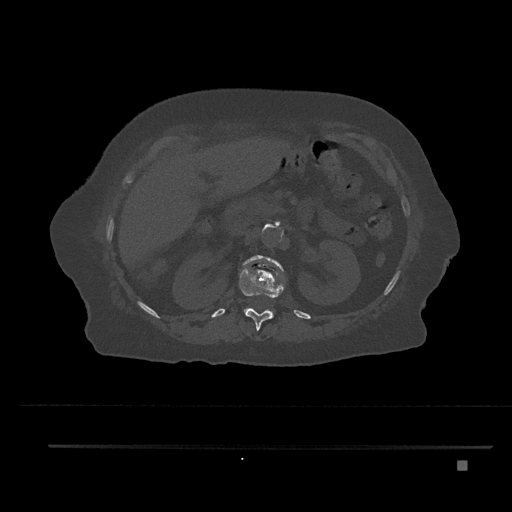
CT including the spine, one axial slice. Slice 250 of 797 in the series (ordered by position). Reconstruction kernel Br40s/3. Bone window (W 1800 / L 400 HU). 0.5 mm slice thickness. 512 × 512 image matrix. Patient: female, 76 years. From the clinical record (not read from this slice): primary cancer: lung.
Outlined on this slice (semi-automatically segmented with operator editing):
- L1 vertebra: bounding box (x1, y1, x2, y2) in pixels: (243, 255, 285, 315)
- T12 vertebra: (239, 268, 284, 331)